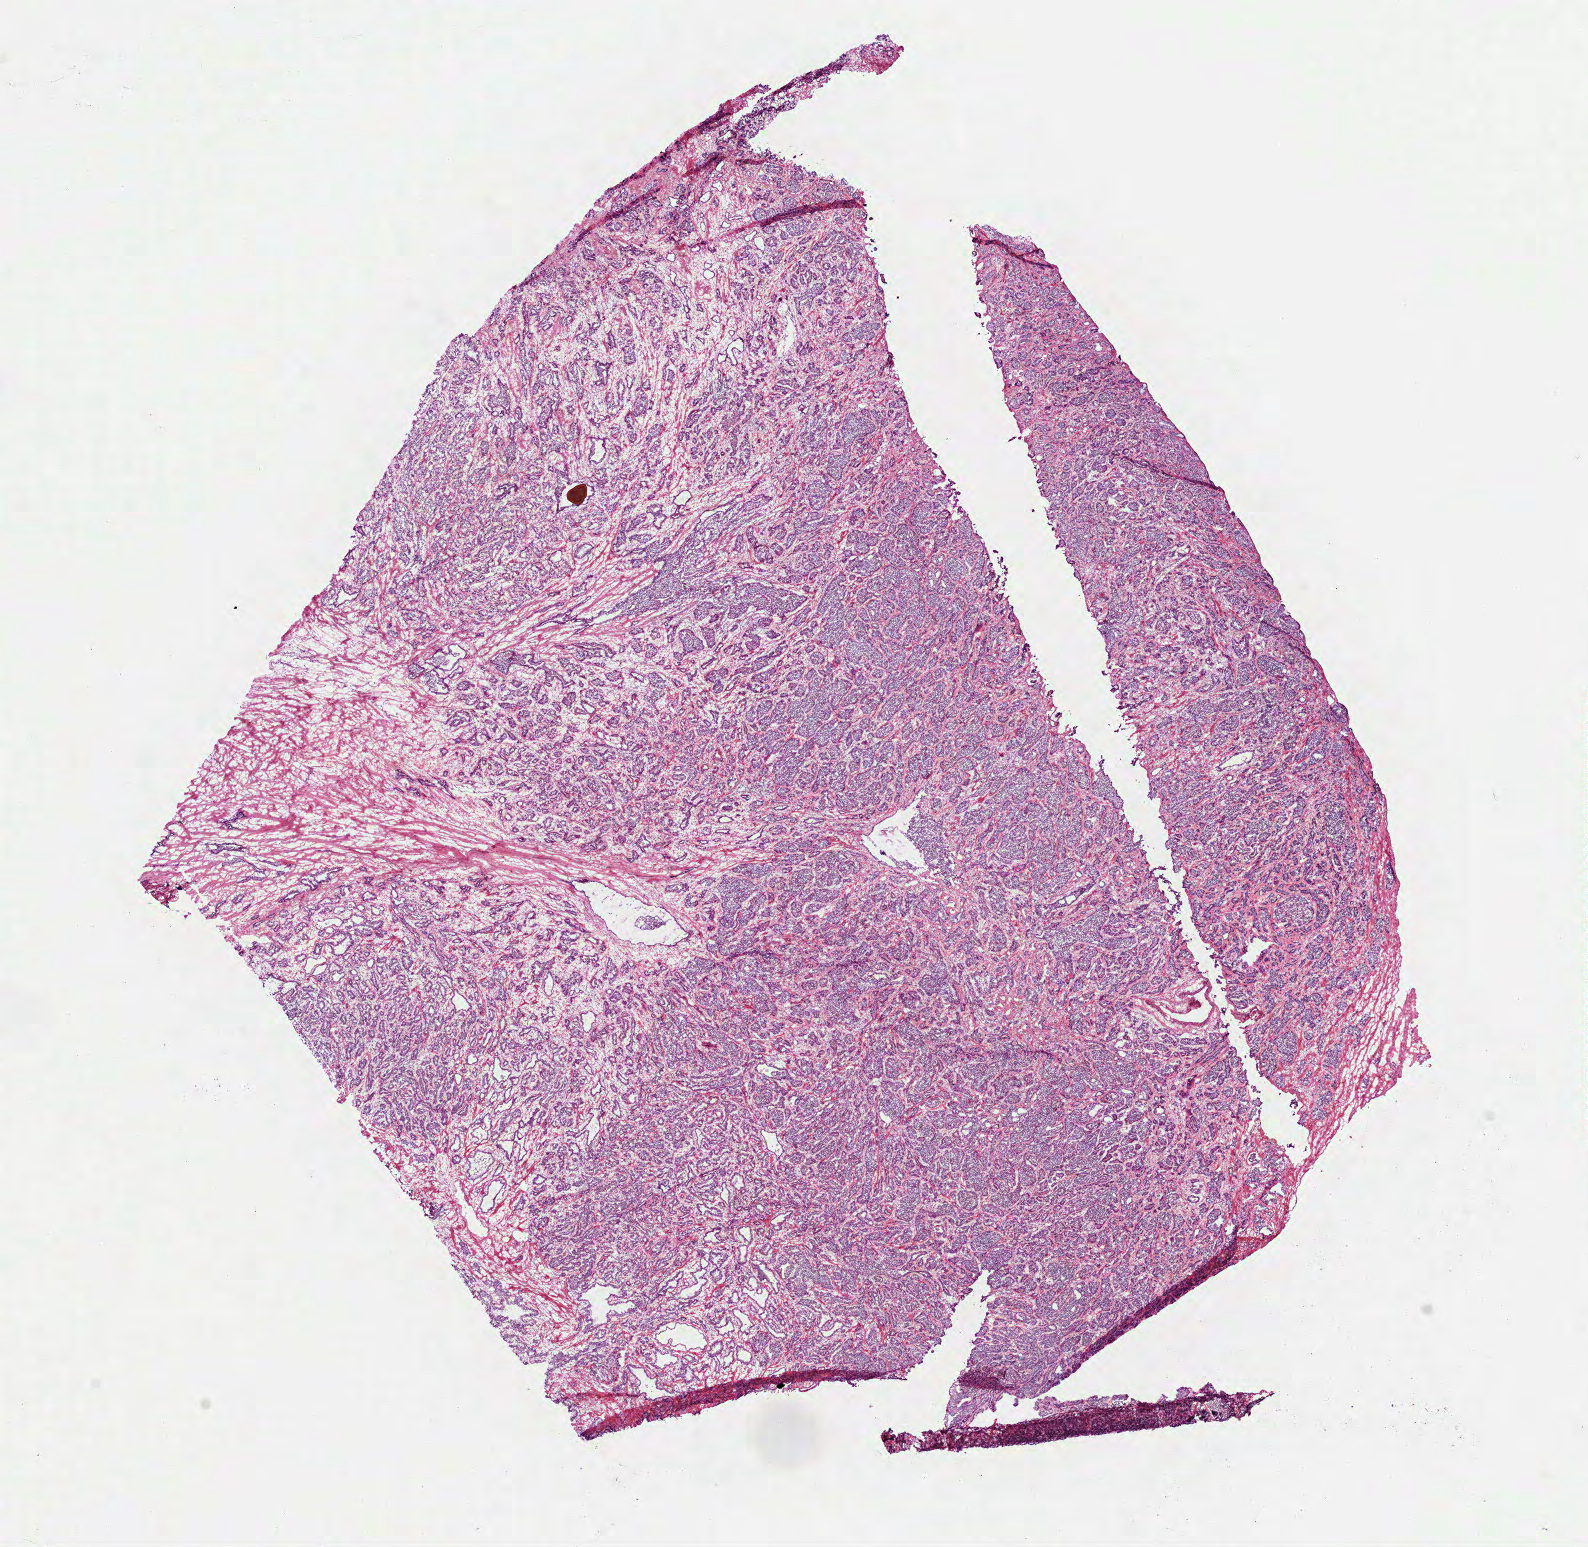
Hematoxylin and eosin (H&E) stained whole-slide image, a low-resolution overview of the entire scanned area, about 12.8 x 12.5 mm. Frozen section from the top of the tissue portion. Prostate, primary tumour sample. Male, age 63 years at initial diagnosis. Gleason score: 7 (4+3). Slide review estimates, as recorded: tumour cells 90%, tumour nuclei 95%, normal cells 3%, stromal cells 7%, necrosis 0%. Infiltration values recorded for this section: lymphocyte infiltration 0%, monocyte infiltration 0%, neutrophil infiltration 0%.
* diagnosis: Acinar cell carcinoma (prostate gland)